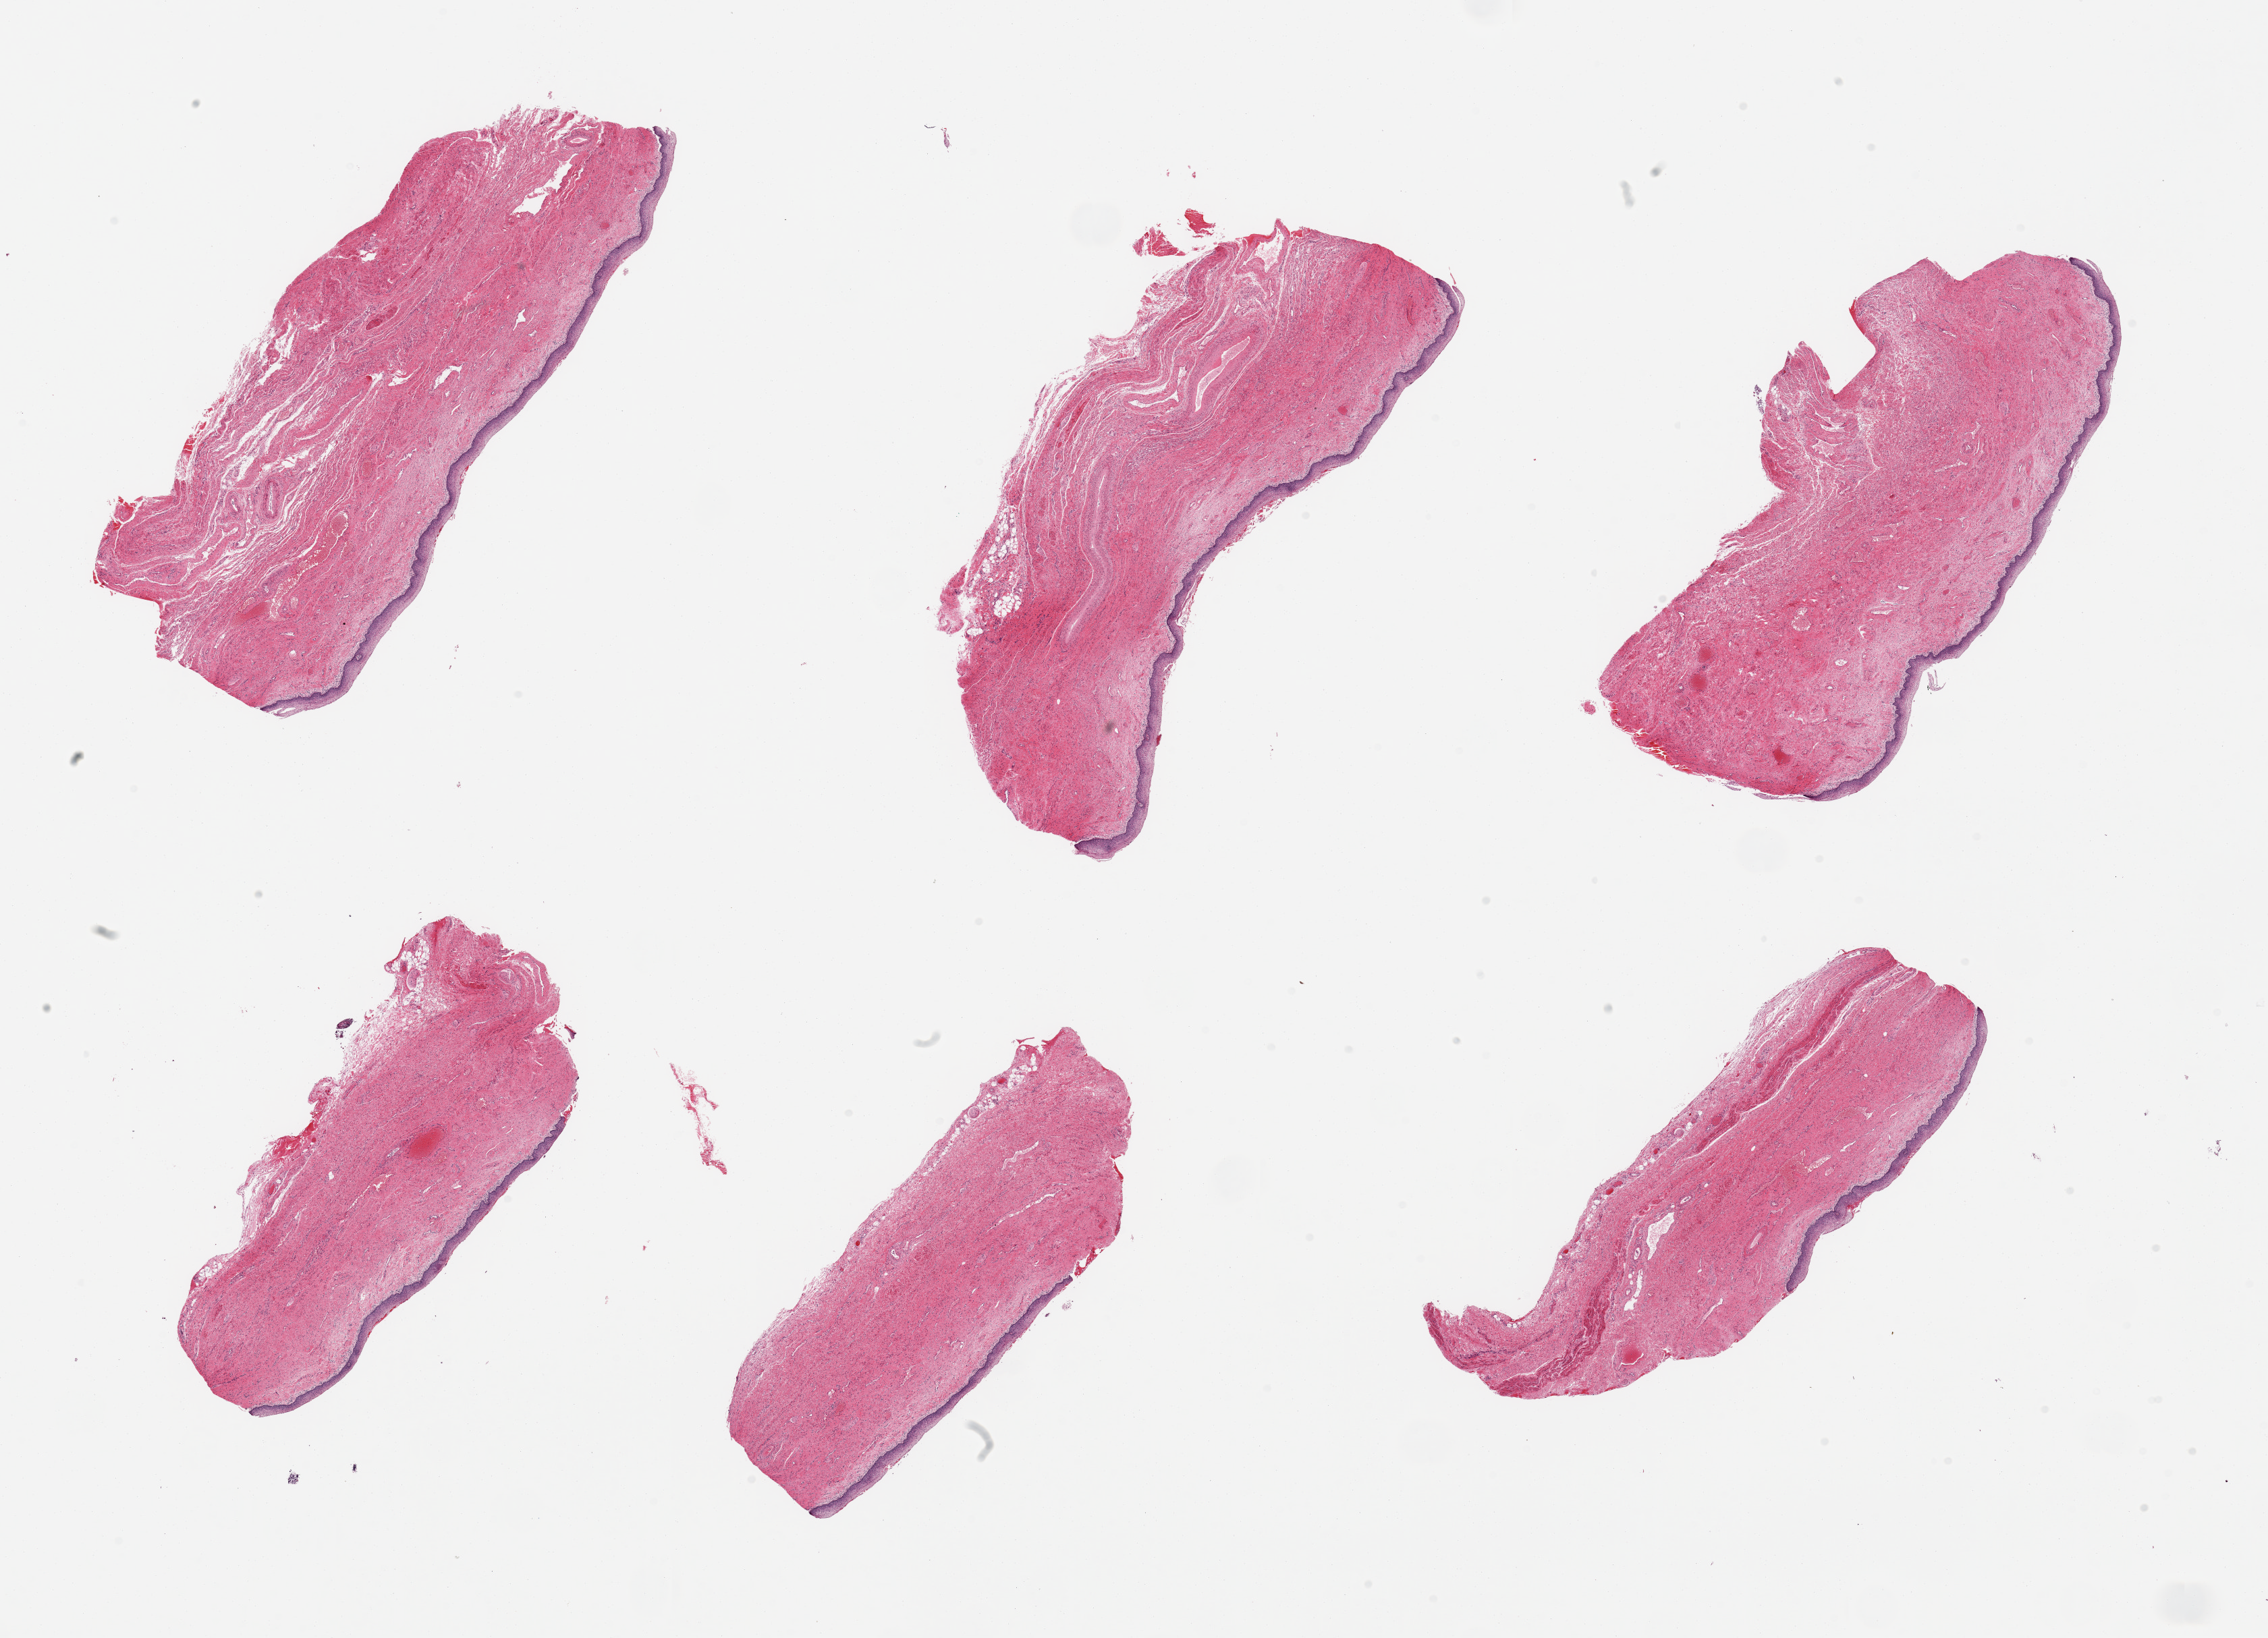
Whole-slide image, hematoxylin and eosin (H&E) stain, brightfield, a low-resolution overview of the entire scanned area, about 26.6 x 19.2 mm (acquisition: 20x scan); PAXgene-fixed paraffin-embedded (PFPE) section; section of vagina (target tissue); donor tissue sample. Female donor.
- reviewer comment on this tissue sample: 6 pieces, squamous mucosa up to ~0.2mm